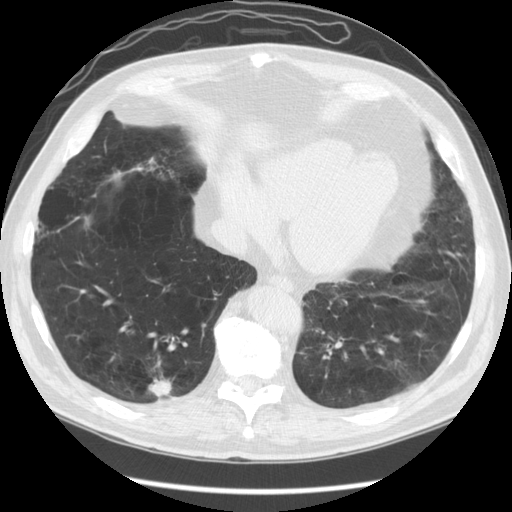
Axial slice from a low-dose chest CT screening exam. First (baseline) screen. Lung window (W 1500 / L -600 HU). Standard (soft-tissue) reconstruction kernel (STANDARD). 120 kVp. Male participant, aged 67 years at enrolment. Former smoker at enrolment.
Expert-annotated lung lesion, bounding box [x1, y1, x2, y2] px = [121, 356, 186, 415]. The screening reader recorded 2 non-calcified nodules or masses ≥4 mm on this exam; which of them this box marks is not recorded. Later outcome: lung cancer diagnosed 78 days after this screen — squamous cell carcinoma, NOS, right lower lobe, moderately differentiated (G2), stage IA (AJCC 6th edition), 23 mm at pathology.